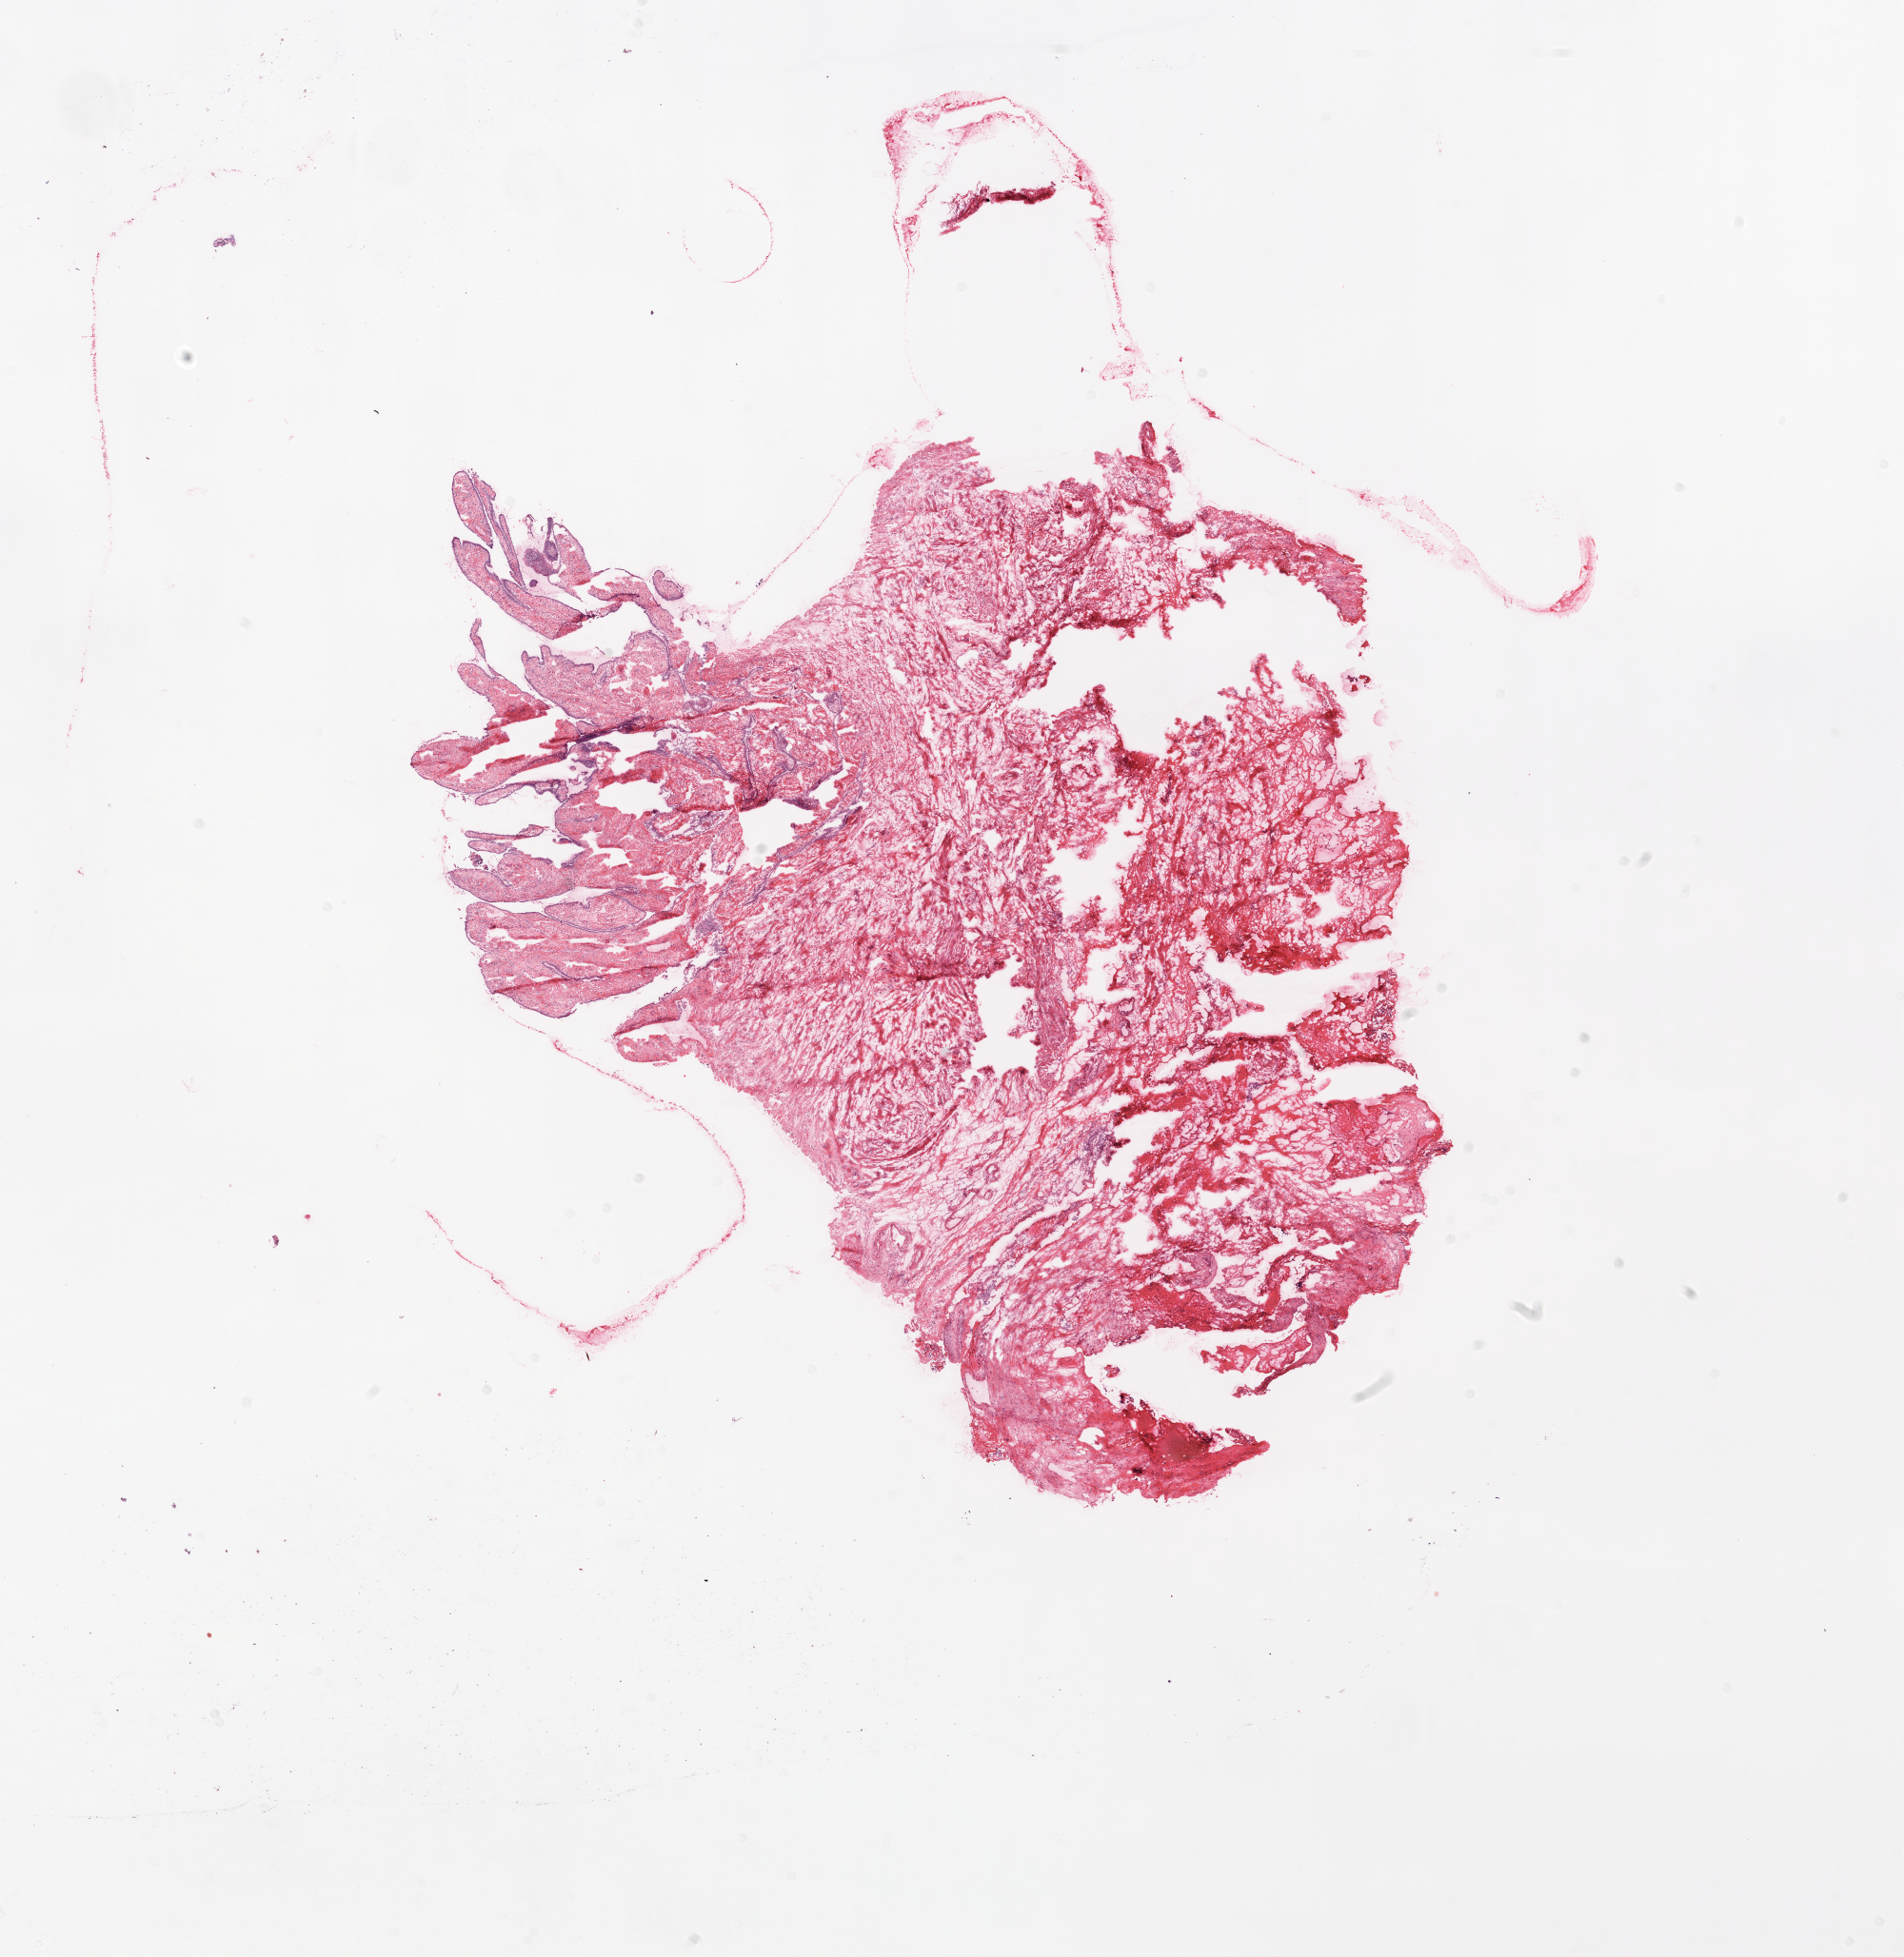
Hematoxylin and eosin (H&E) stained whole-slide image, shown as a low-resolution overview of the whole scanned area (about 16.0 x 16.5 mm), frozen section from the top of the tissue portion, ovary, solid tissue normal (non-tumour tissue) sample. Female, age 81 years at initial diagnosis.
- this section: solid tissue normal (non-tumour) sample from the same patient
- patient diagnosis: Serous cystadenocarcinoma, NOS